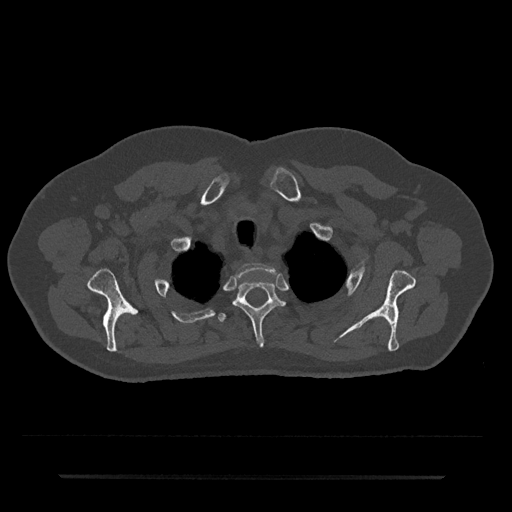
CT including the spine, one axial slice; slice 605 of 797 in the series (ordered by position); reconstruction kernel Br40s/3; bone window (W 1800 / L 400 HU); 0.5 mm slice thickness; 512 × 512 image matrix. Male patient, age 69 years. Case-level facts recorded for this patient, not image findings: primary cancer: prostate.
Structures marked on this image (semi-automatically segmented with operator editing):
- T1 vertebra: bounding box <236,263,278,277> (left, top, right, bottom; pixels)
- T2 vertebra: <233,281,285,346>
- T3 vertebra: <218,313,226,322>